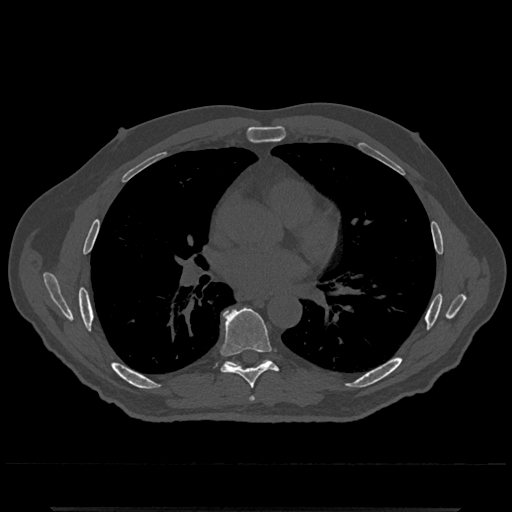
CT including the spine, one axial slice. Position 714 of 797 along the scan axis. Reconstruction kernel Br40s/3. Bone window (W 1800 / L 400 HU). 0.5 mm slice thickness. 512 × 512 image matrix. Patient: male, 67 years. Case-level facts recorded for this patient, not image findings: primary cancer: prostate.
Annotated regions visible in this slice (semi-automatically segmented with operator editing):
- T6 vertebra: bounding box <249,396,254,401> (left, top, right, bottom; pixels)
- T7 vertebra: <220,308,278,389>
- T8 vertebra: <224,359,269,367>